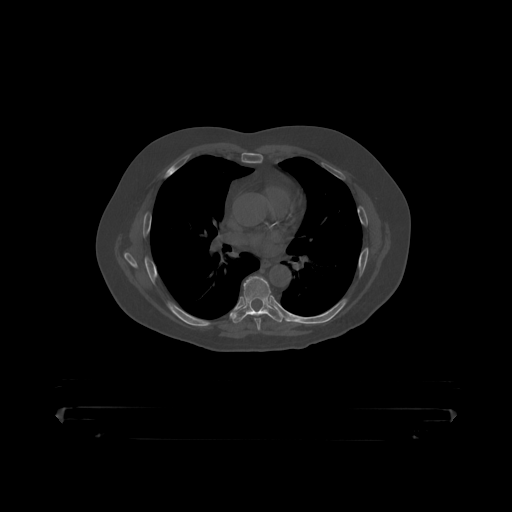
CT including the spine, one axial slice. Reconstruction kernel STANDARD. Bone window (W 1800 / L 400 HU). 1.25 mm slice thickness. 512 × 512 image matrix, field of view 650 × 650 mm. Male patient, age 60 years. From the clinical record (not read from this slice): primary cancer: prostate.
Outlined on this slice (semi-automatically segmented with operator editing):
- T7 vertebra: box from (x=236, y=277) to (x=280, y=318) px